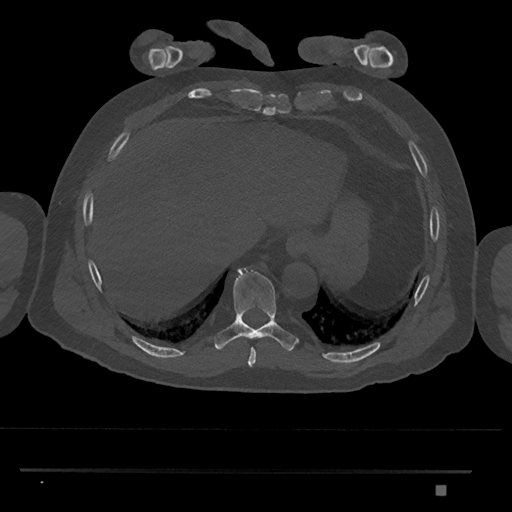
CT including the spine, one axial slice; position 1059 of 1134 along the scan axis; 120 kVp; bone window (W 1800 / L 400 HU); 0.5 mm slice thickness; 512 × 512 image matrix, field of view 429 × 429 mm. Male patient, age 65 years. From the clinical record (not read from this slice): primary cancer: prostate.
Structures marked on this image (semi-automatically segmented with operator editing):
- T8 vertebra: bounding box <248,347,256,367> (left, top, right, bottom; pixels)
- T9 vertebra: <214,267,299,352>